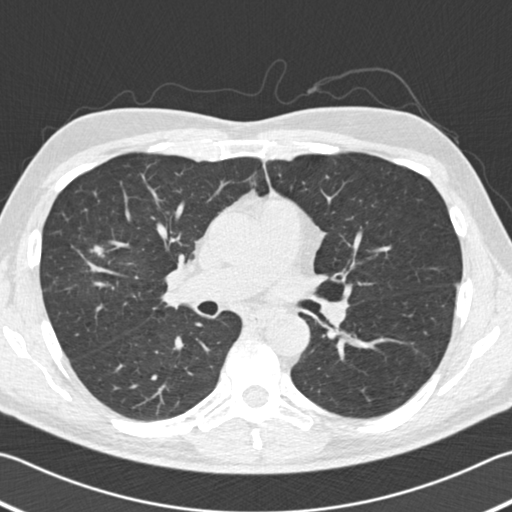
Low-dose screening chest CT, one axial slice. Position 108 of 182 along the scan axis. Reconstruction kernel B30f. 120 kVp. Lung window (W 1500 / L -600 HU). 2 mm slice thickness. 512 × 512 image matrix.
Annotated regions visible in this slice (outlined manually by an expert reader):
- lesion 1 (tumor, upper lobe of right lung): bounding box [x1, y1, x2, y2] px = [90, 245, 104, 257]